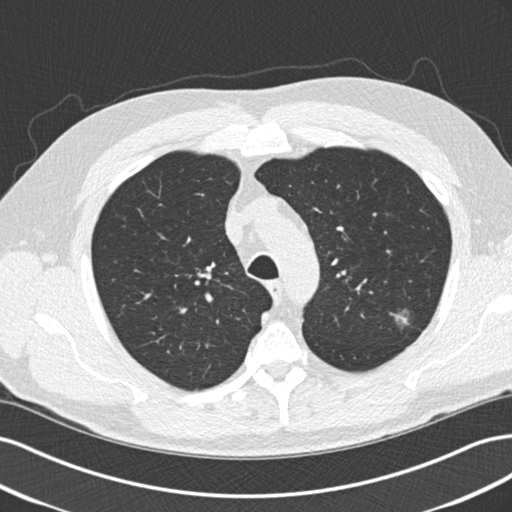
Axial slice from a low-dose chest CT screening exam; second screening round (one year after baseline); lung window (W 1500 / L -600 HU); 2 mm slice thickness; standard (soft-tissue) reconstruction kernel (B30f); slice 48 of 209 in the series; 512 × 512 image matrix, field of view 360 × 360 mm. Male participant, aged 65 years at enrolment. Former smoker at enrolment.
Expert reader's lesion annotation, box from (x=386, y=304) to (x=425, y=344) px. Reader record for this screening exam (exam-level; its link to the box is not recorded): non-calcified nodule or mass ≥4 mm, left upper lobe, 10 × 9 mm, poorly defined margins, mixed attenuation, pre-existing on the prior screen: yes; interval growth: no. Official screen result: positive, other. Lung cancer was diagnosed 221 days after this screen: adenocarcinoma, NOS, left upper lobe, poorly differentiated (G3), stage IA (AJCC 6th edition), 13 mm at pathology.